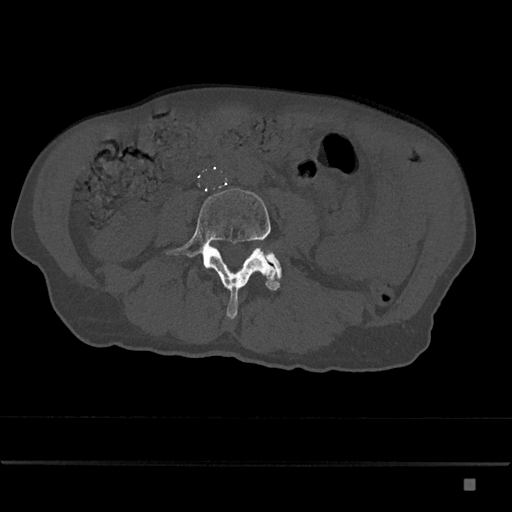
CT including the spine, one axial slice; slice 335 of 797 in the series (ordered by position); reconstruction kernel Br40s/3; bone window (W 1800 / L 400 HU); 512 × 512 image matrix. Patient: male, 72 years. From the clinical record (not read from this slice): primary cancer: prostate.
Outlined on this slice (semi-automatic segmentation, software-assisted and operator-edited):
- L4 vertebra: bounding box [x1, y1, x2, y2] px = [166, 189, 282, 319]
- L5 vertebra: [267, 254, 282, 274]